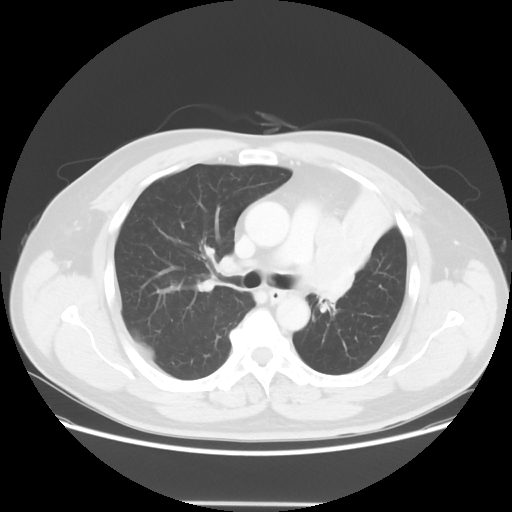
Chest CT, one axial slice. Position 39 of 62 along the scan axis. 120 kVp. Lung window (W 1500 / L -600 HU). 5 mm slice thickness. 512 × 512 image matrix, field of view 403 × 403 mm. Patient: male, 49 years. Case-level facts recorded for this patient, not image findings: clinical TNM (as recorded): T3 N3 M1c.
Structures marked on this image (bounding box drawn by a radiologist):
- lung tumour (recorded histology: squamous cell carcinoma): bounding box (x1, y1, x2, y2) in pixels: (306, 209, 395, 321)